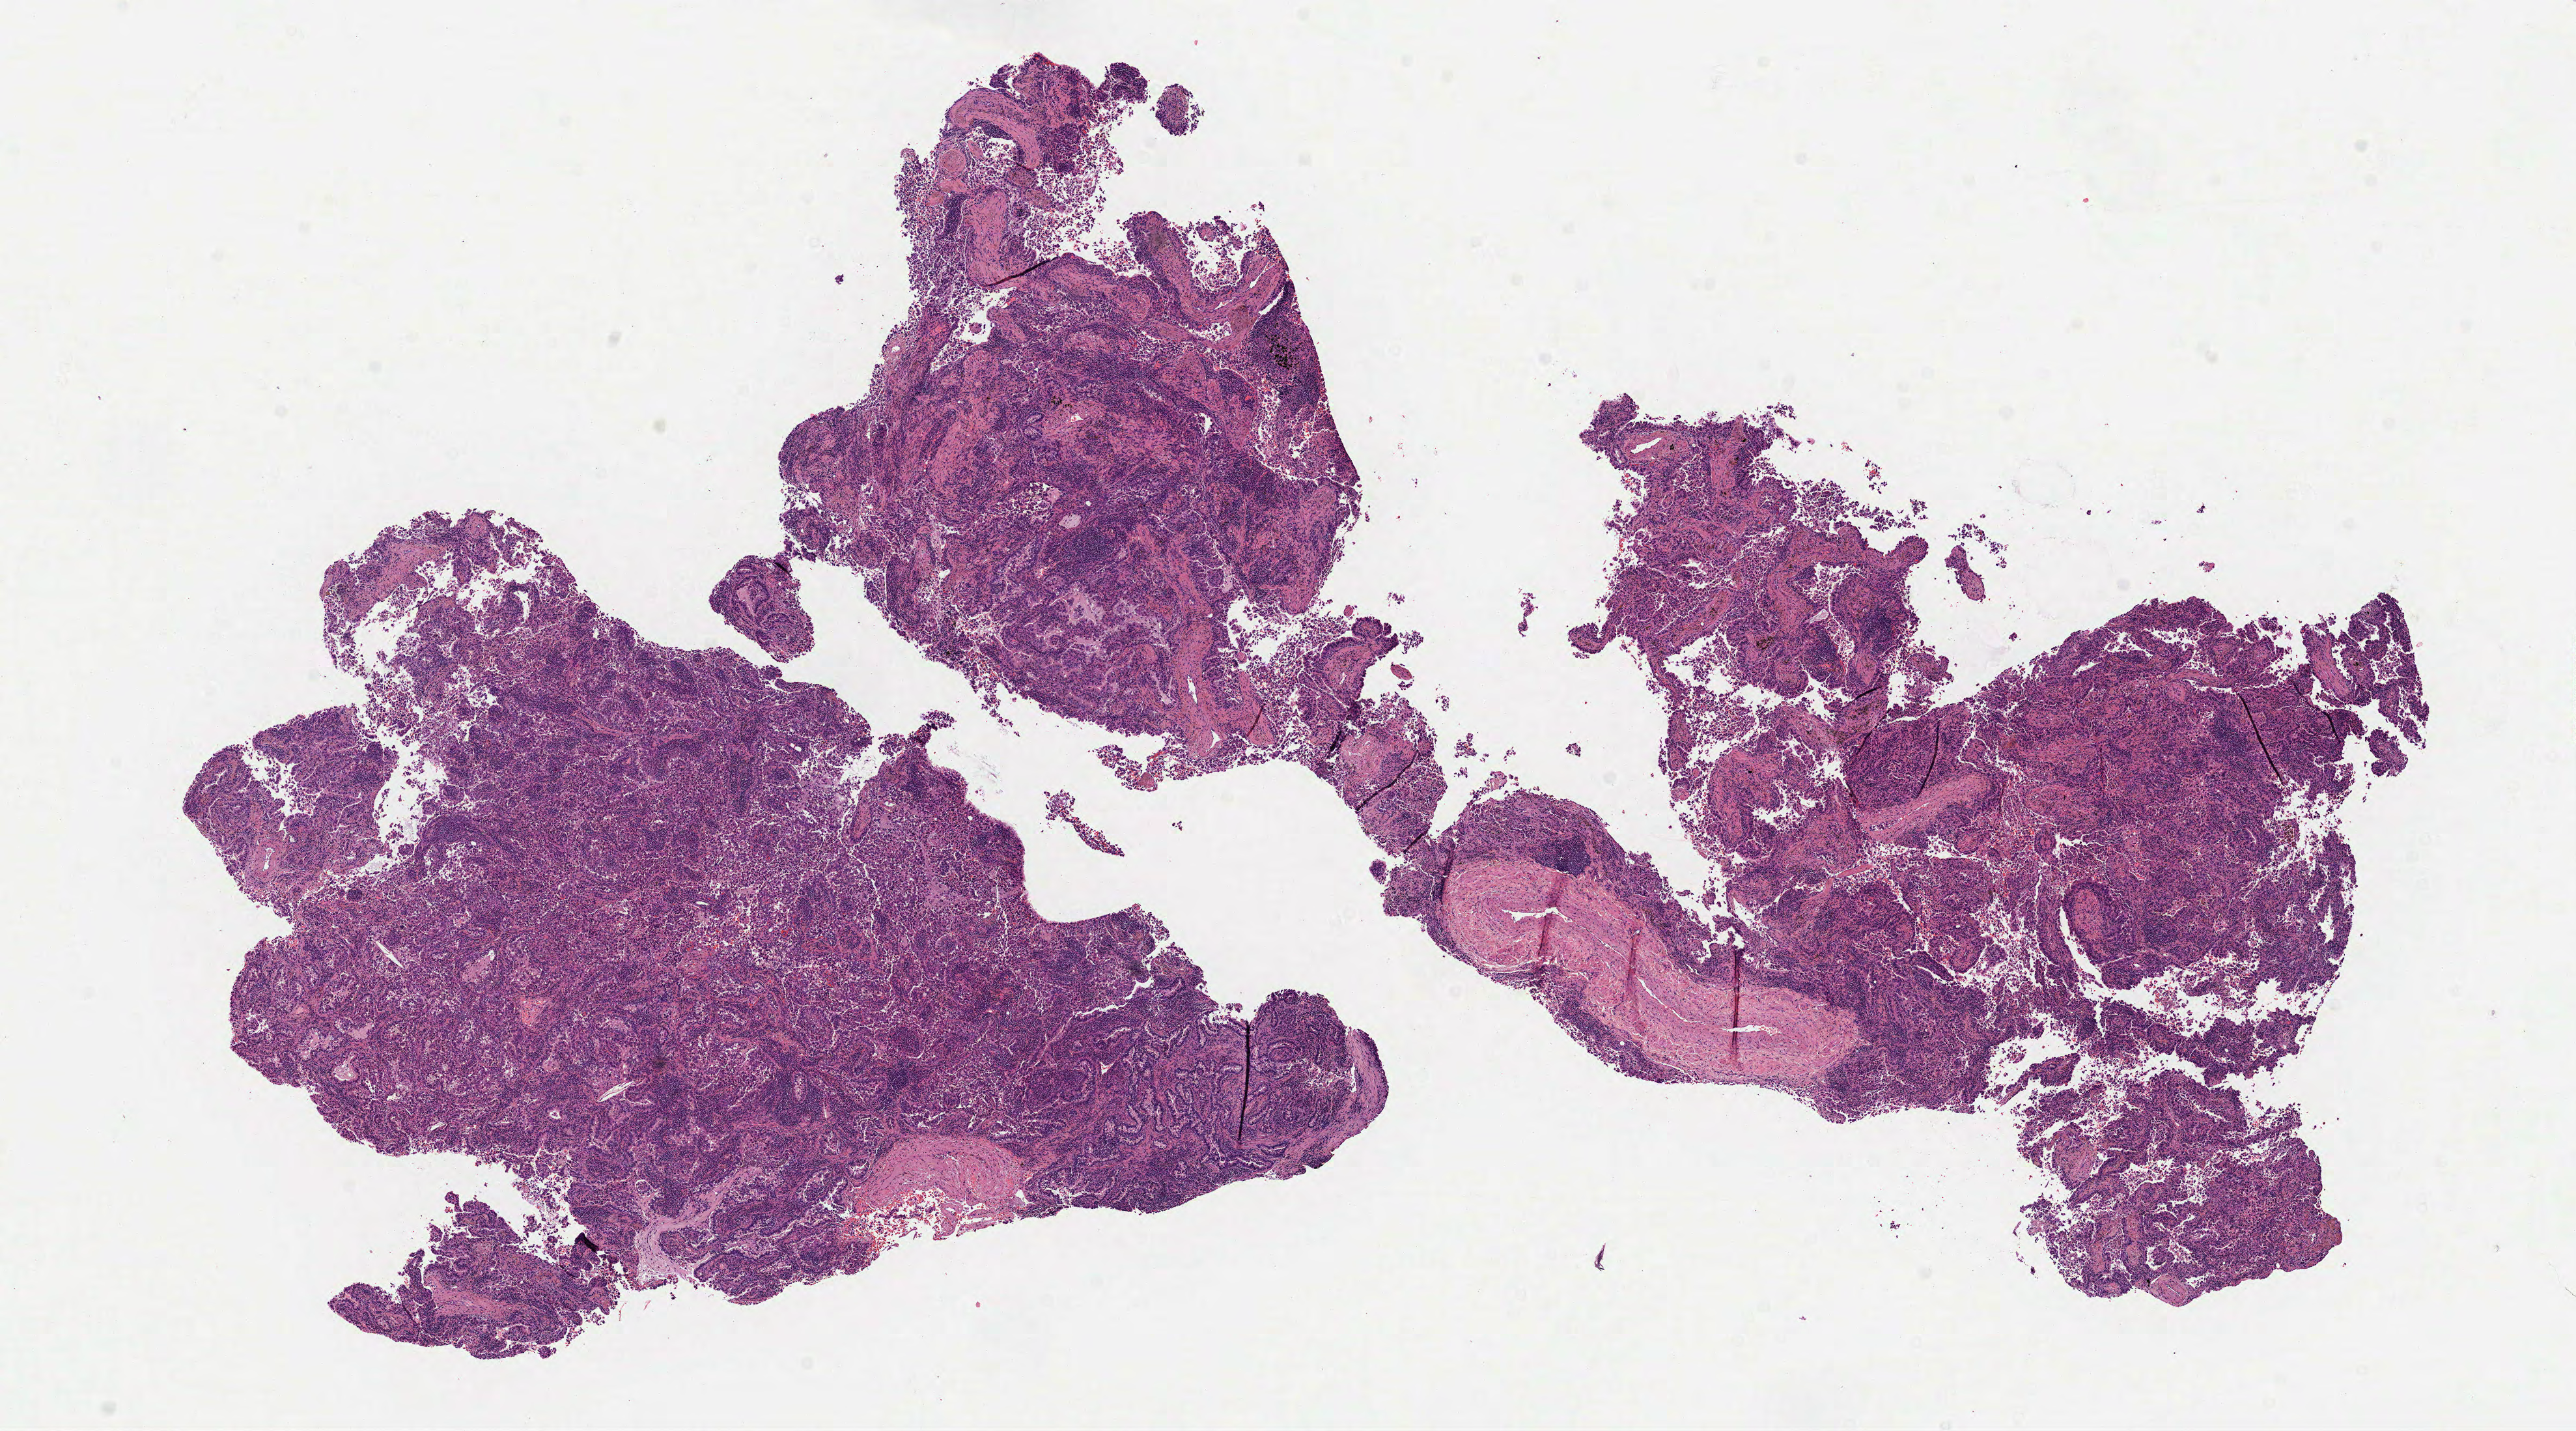
Whole-slide histology image, H&E-stained — low-resolution overview of the scanned area, about 16.0 x 8.9 mm (acquisition: 40x scan); frozen section from the top of the tissue portion; sample: primary tumour, lung. Patient: male, age at initial diagnosis 62 years. Composition of this section per pathologist review: tumour cells 100%, tumour nuclei 61%, normal cells 0%, stromal cells 0%, necrosis 0%. Inflammatory infiltration, as recorded: lymphocyte infiltration 25%, monocyte infiltration 5%, neutrophil infiltration 0%.
- laterality: right
- diagnosis: Adenocarcinoma, NOS (upper lobe, lung)
- AJCC pathologic stage: IIB (7th edition)